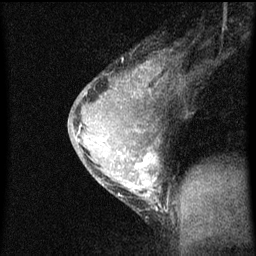
Breast MRI (dynamic contrast-enhanced), one sagittal slice; position 41 of 60 along the scan axis; dynamic contrast-enhanced series, image 2 of 3 at this slice position (ordered by acquisition); 1.5 T; TE 4.2 ms, TR 8 ms; 256 × 256 image matrix, field of view 180 × 180 mm. Female patient, age 33 years.
Annotated regions visible in this slice (semi-automatically segmented with operator editing):
- analysis volume of interest (the breast-tissue region the enhancement analysis was run in; not a lesion): bounding box [x1, y1, x2, y2] px = [68, 62, 177, 211]
- tumour enhancement mask (voxels above the 70 % enhancement threshold inside the analysis volume of interest): [79, 64, 161, 209]